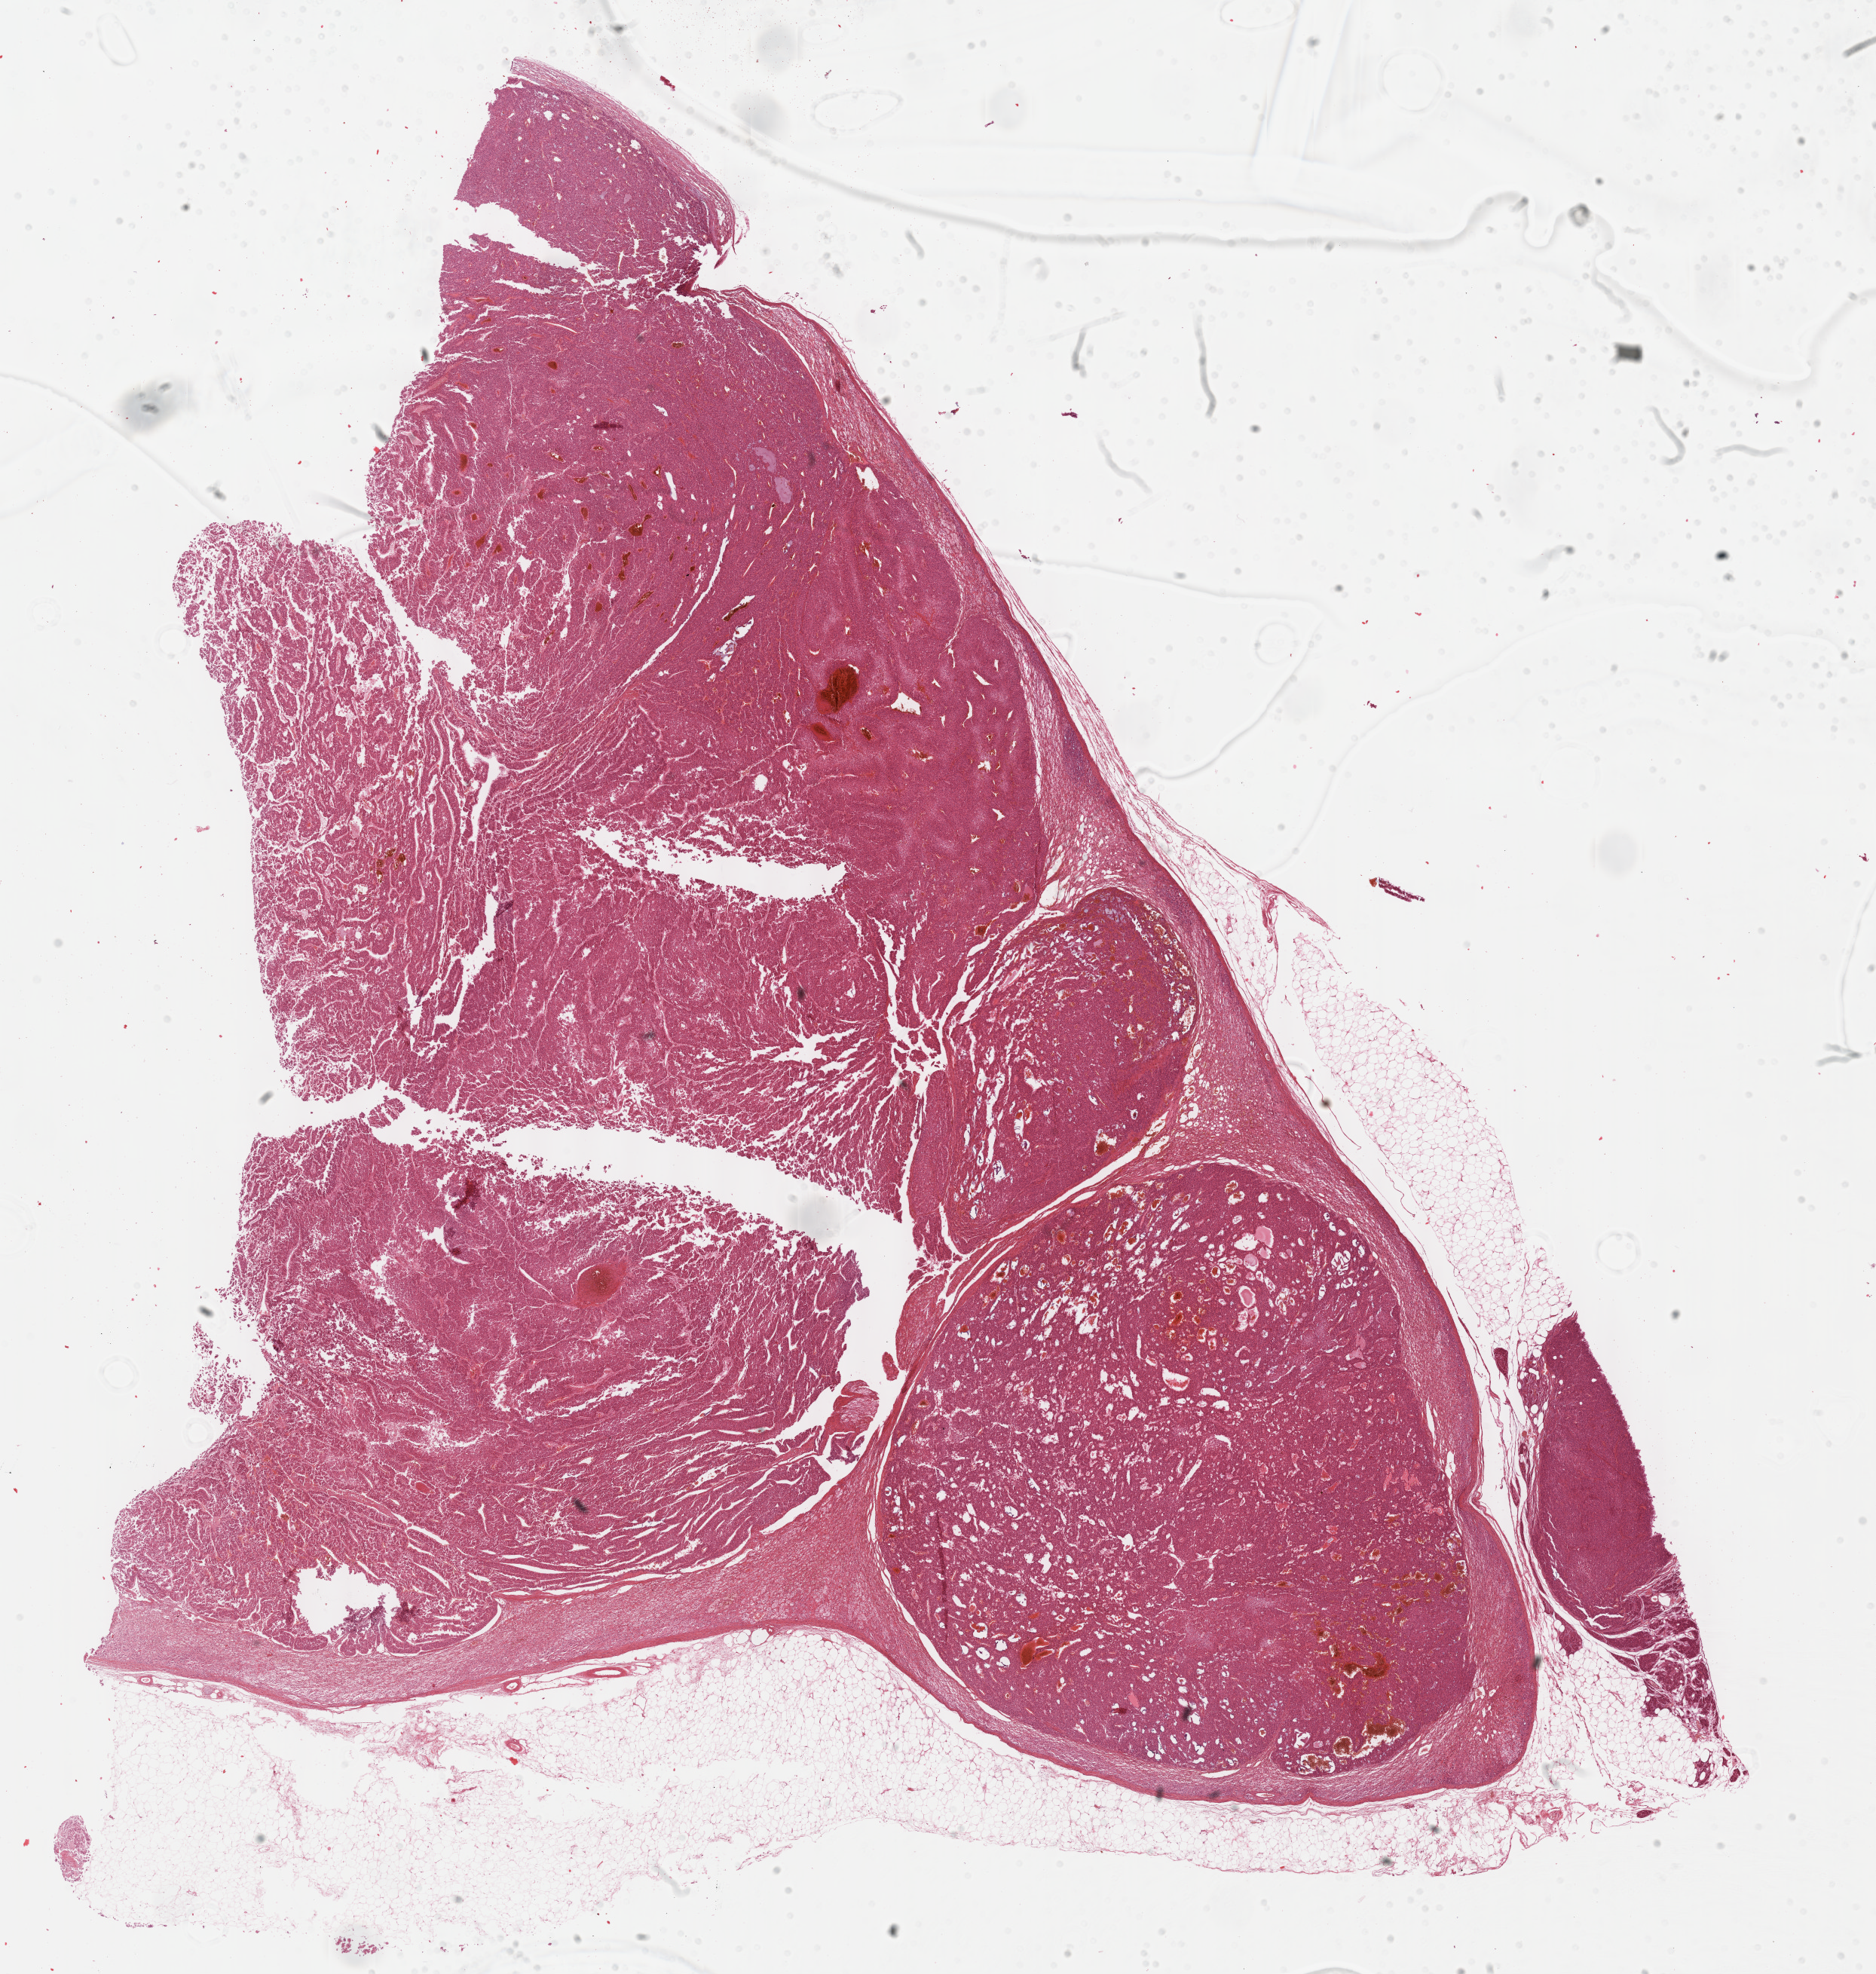
Digitized H&E tissue section (whole slide) — shown as a low-resolution overview of the whole scanned area (about 20.1 x 21.2 mm, from a 40x scan); formalin-fixed paraffin-embedded (FFPE) diagnostic section; primary tumour sample from the adrenal cortex. Male patient; age at initial diagnosis 61 years.
Pathologic diagnosis: Adrenal cortical carcinoma (cortex of adrenal gland). Lymph nodes positive (case pathology): 6 of 8 examined. Laterality: left.